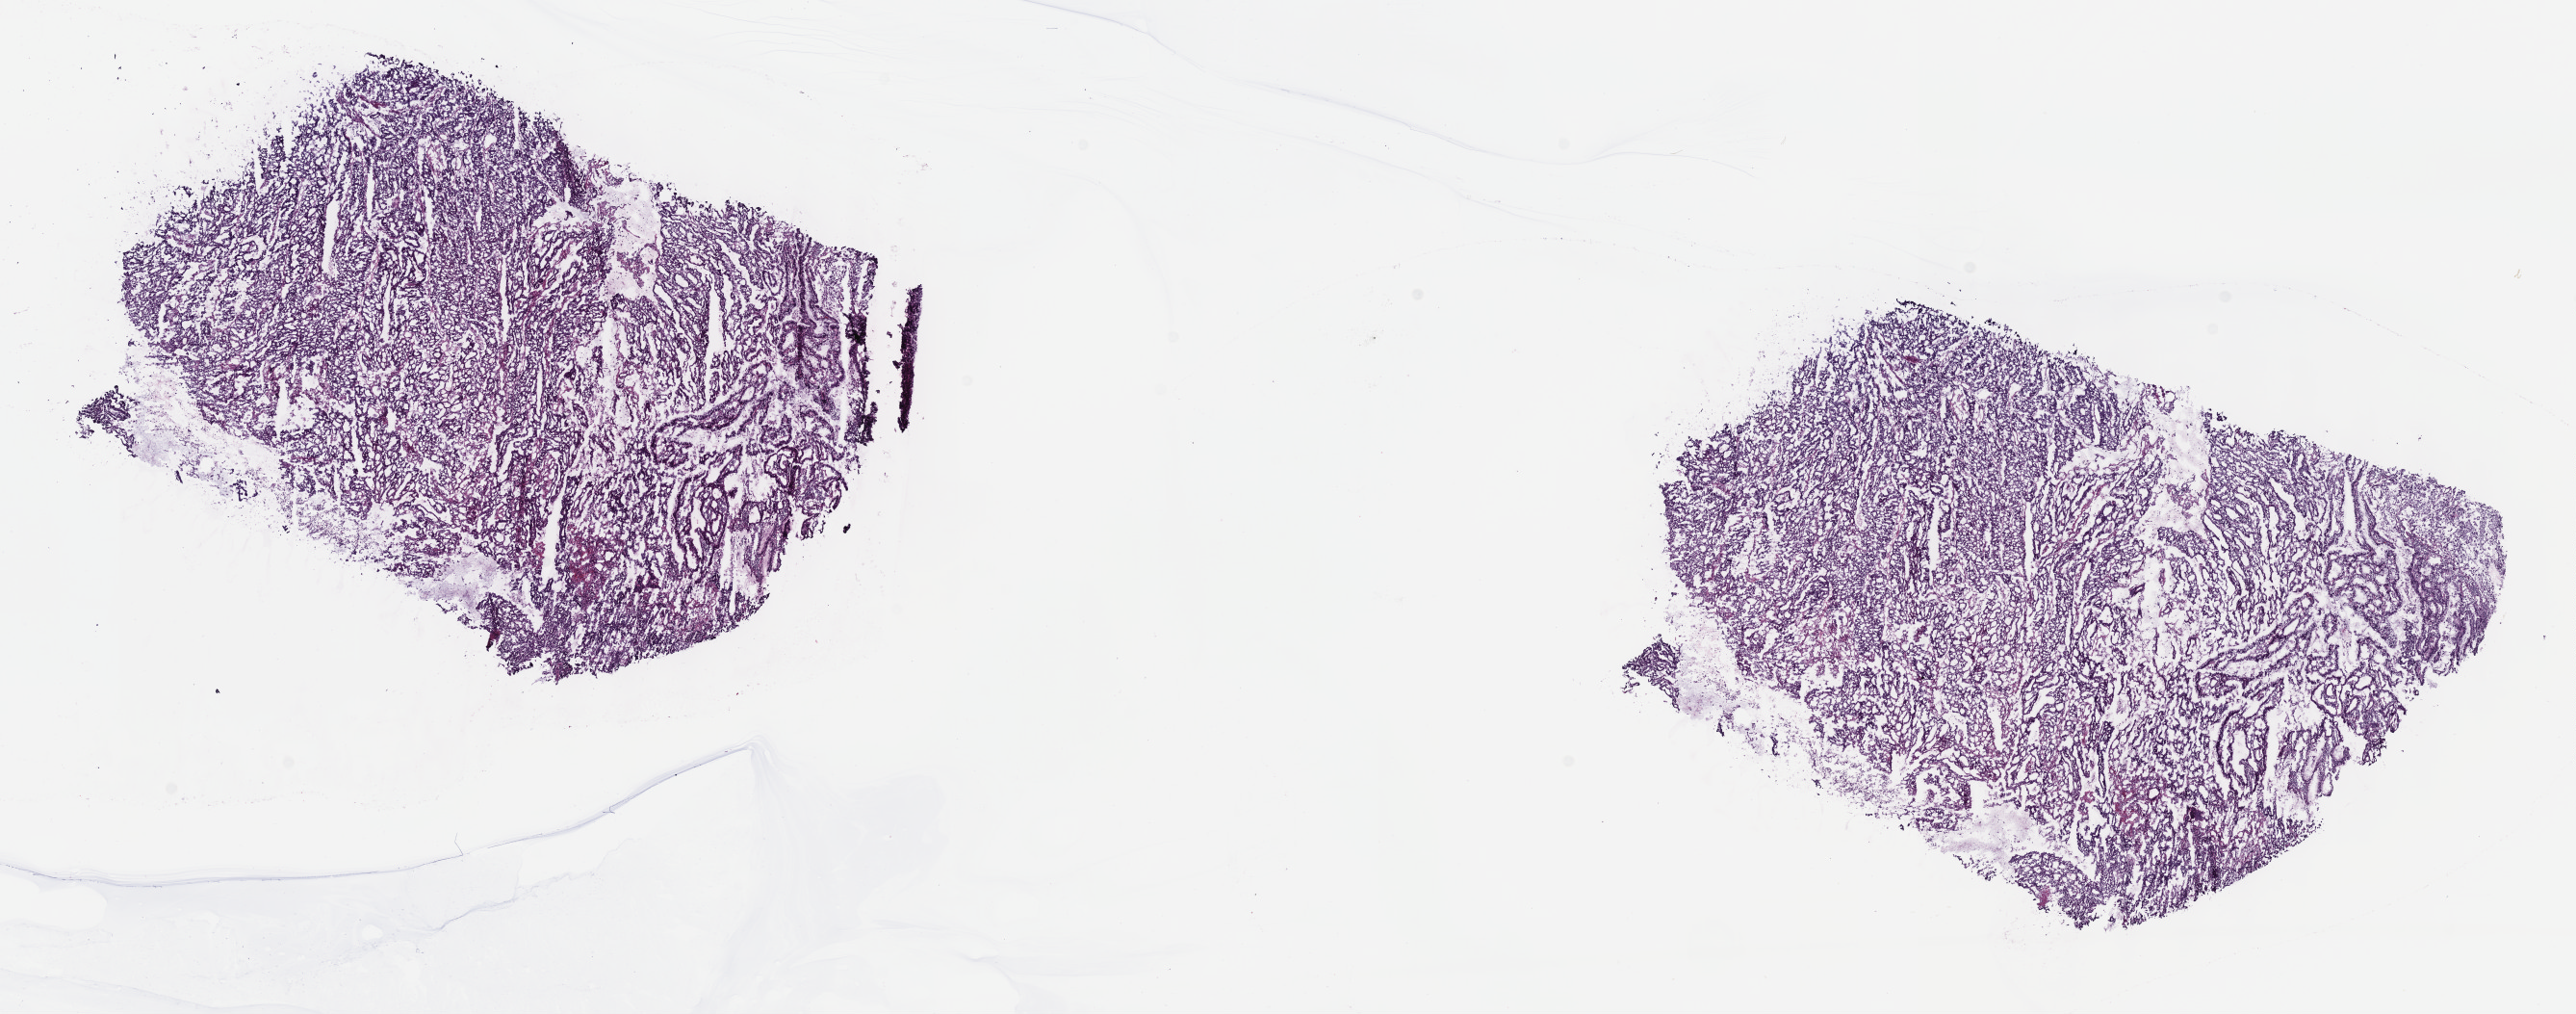
Hematoxylin and eosin (H&E) stained whole-slide image — whole scanned area (about 21.6 x 8.5 mm) shown as a low-resolution overview. Frozen section from the top of the tissue portion. Primary tumour sample from the stomach. Male, age 68 years at initial diagnosis. Histologic grade: G2 (moderately differentiated). Slide review estimates, as recorded: tumour cells 90%, tumour nuclei 95%, normal cells 0%, stromal cells 10%, necrosis 0%. Inflammatory infiltration, as recorded: lymphocyte infiltration 0%, monocyte infiltration 0%, neutrophil infiltration 0%.
TNM: T4a N1 M0. AJCC pathologic stage: IIIA. Pathologic diagnosis: Mucinous adenocarcinoma (body of stomach).